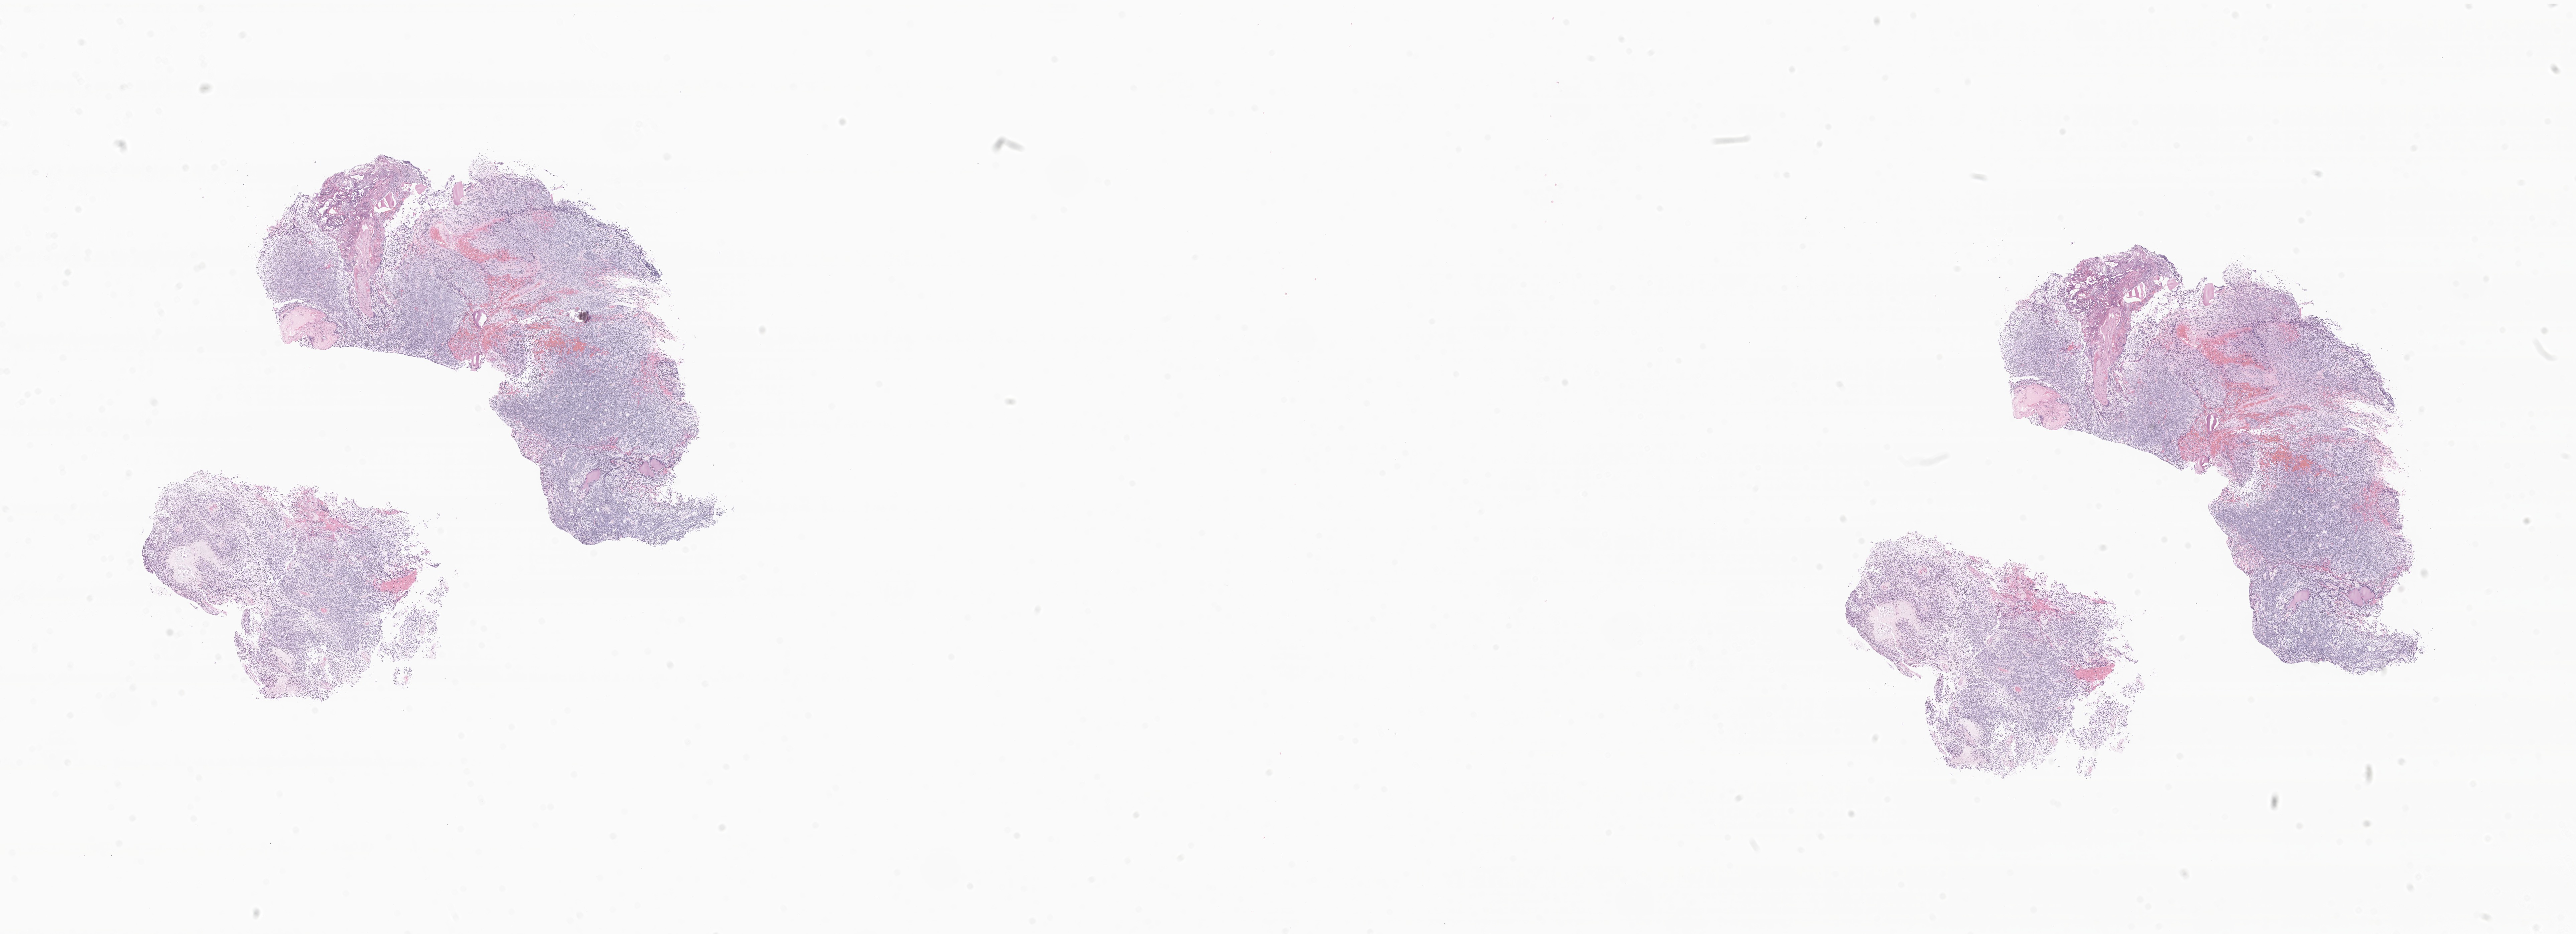
Hematoxylin and eosin (H&E) whole-slide image of tumor tissue from the cerebral ventricle, whole scanned area (about 32.5 x 11.8 mm) shown as a low-resolution overview, formalin-fixed, paraffin-embedded (FFPE) tissue. Patient female; age 109 months (9 years 1 month).
Diagnosis: Neoplasm, malignant.